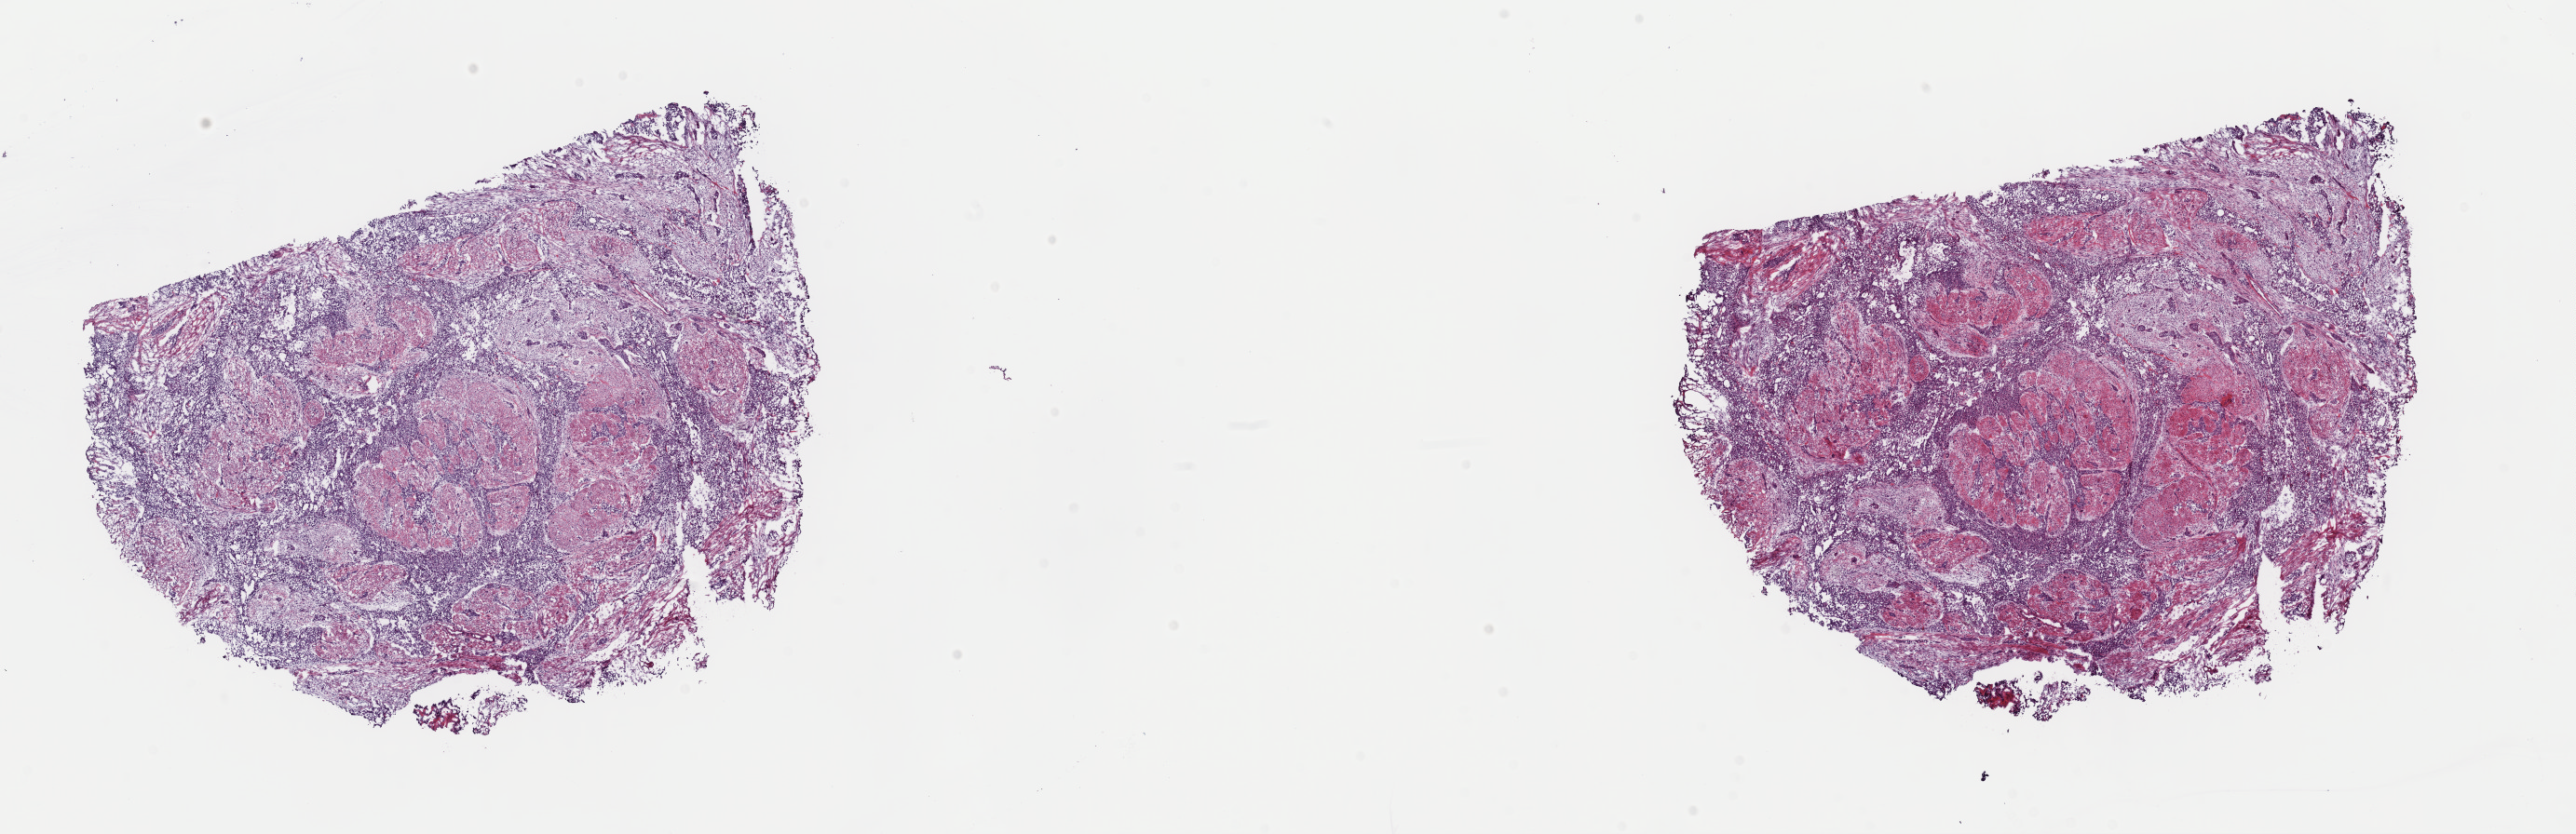
H&E whole-slide image, whole scanned area (about 21.9 x 7.1 mm, acquisition: 40x scan) shown as a low-resolution overview. Frozen section from the top of the tissue portion. Primary tumour sample from the bladder. Male patient; age at initial diagnosis 76 years. Histologic grade: high grade. Composition of this section per pathologist review: tumour cells 70%, tumour nuclei 70%, normal cells 0%, stromal cells 30%, necrosis 0%. Inflammatory infiltration, as recorded: lymphocyte infiltration 3%, monocyte infiltration 2%, neutrophil infiltration 3%.
Histologic diagnosis: Transitional cell carcinoma (posterior wall of bladder). AJCC pathologic stage: III (7th edition).